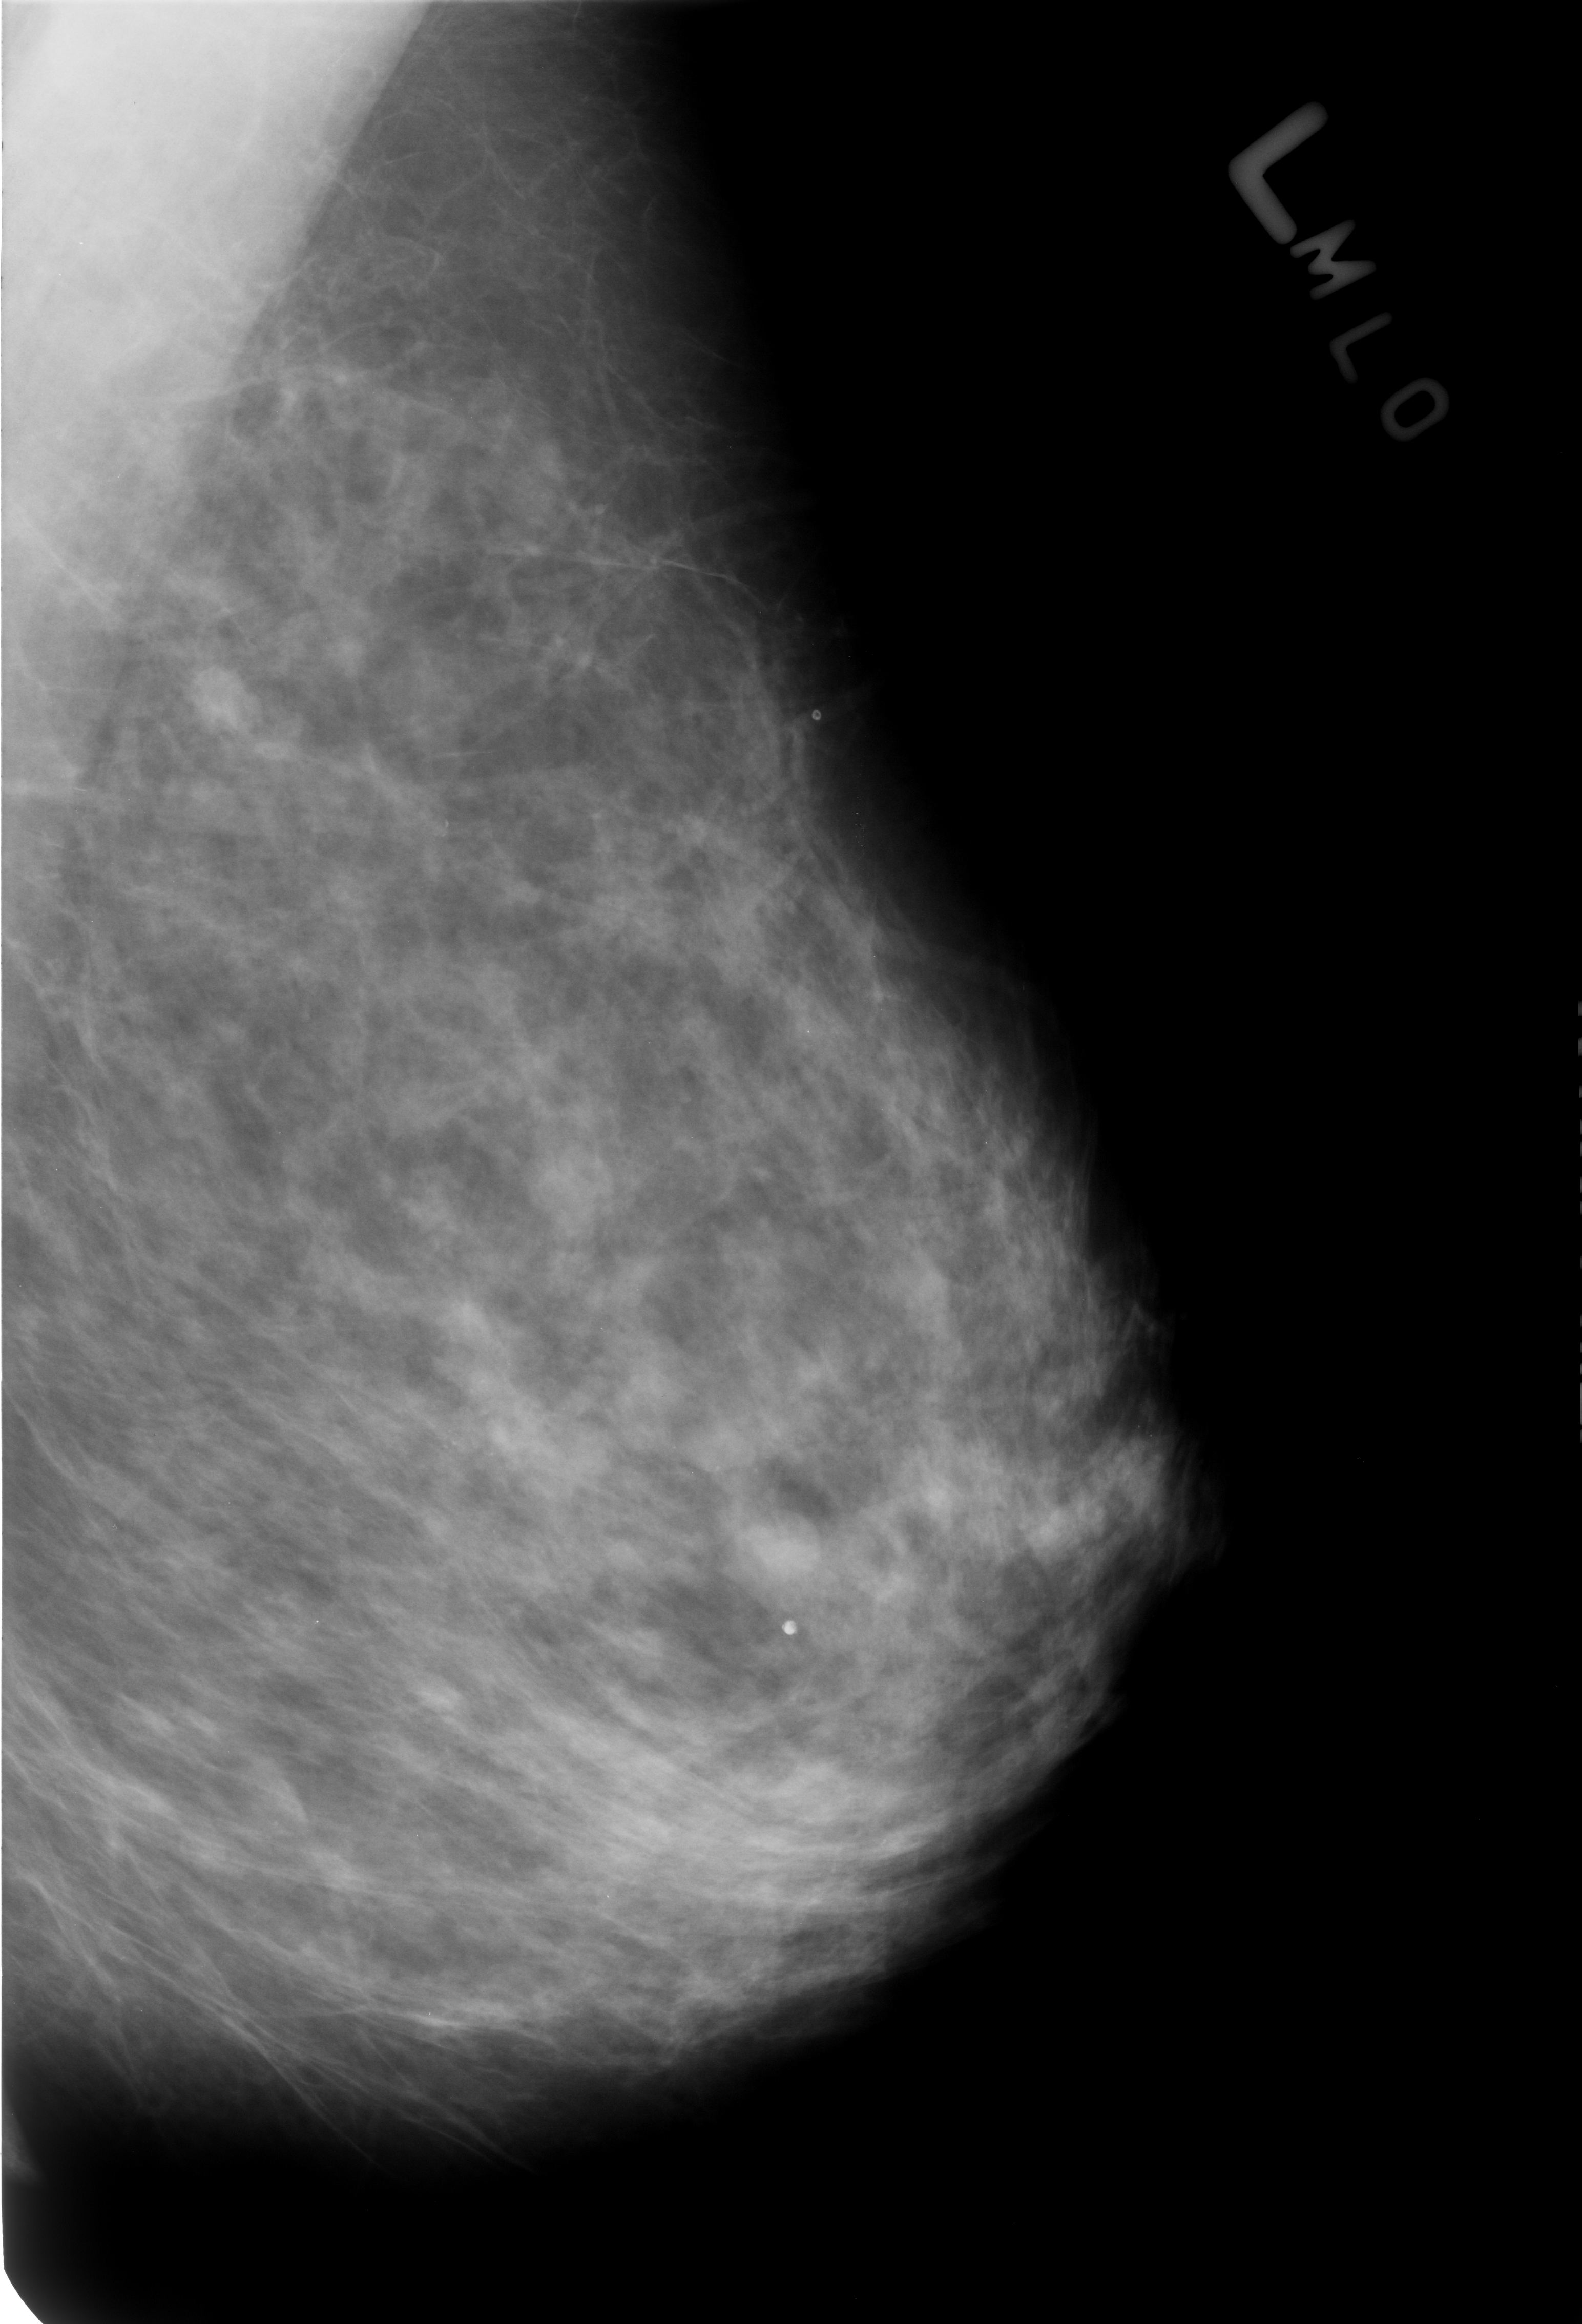
Scanned film-screen mammogram; left breast; MLO view.
Marked findings (only marked abnormalities are described; nothing is implied about the rest of the image): Finding 1 of 2: calcifications, morphology coarse / round and regular / lucent center; BI-RADS assessment category 2; benign; no additional work-up was recommended (benign without callback). Finding 2 of 2: calcifications, morphology coarse / round and regular / lucent center; BI-RADS assessment category 2; benign without callback (not worked up further).